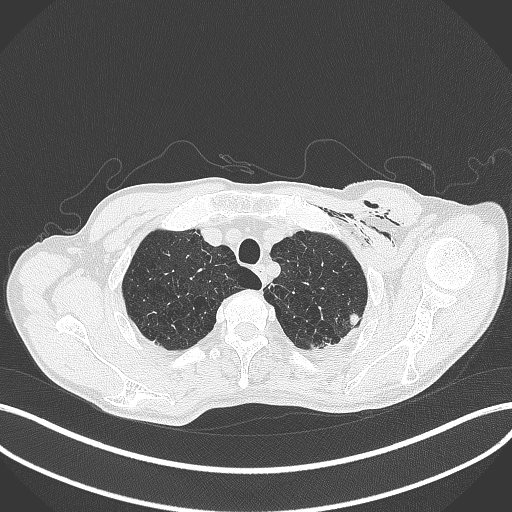
Chest CT, one axial slice; slice 360 of 457 in the series (ordered by position); reconstruction kernel B70f; lung window (W 1500 / L -600 HU); 512 × 512 image matrix, field of view 400 × 400 mm. Patient: male, 58 years. From the clinical record (not read from this slice): clinical TNM (as recorded): T3 N0 M0.
Outlined on this slice (bounding box drawn by a radiologist):
- lung tumour (recorded histology: adenocarcinoma): bounding box <348,310,362,327> (left, top, right, bottom; pixels)